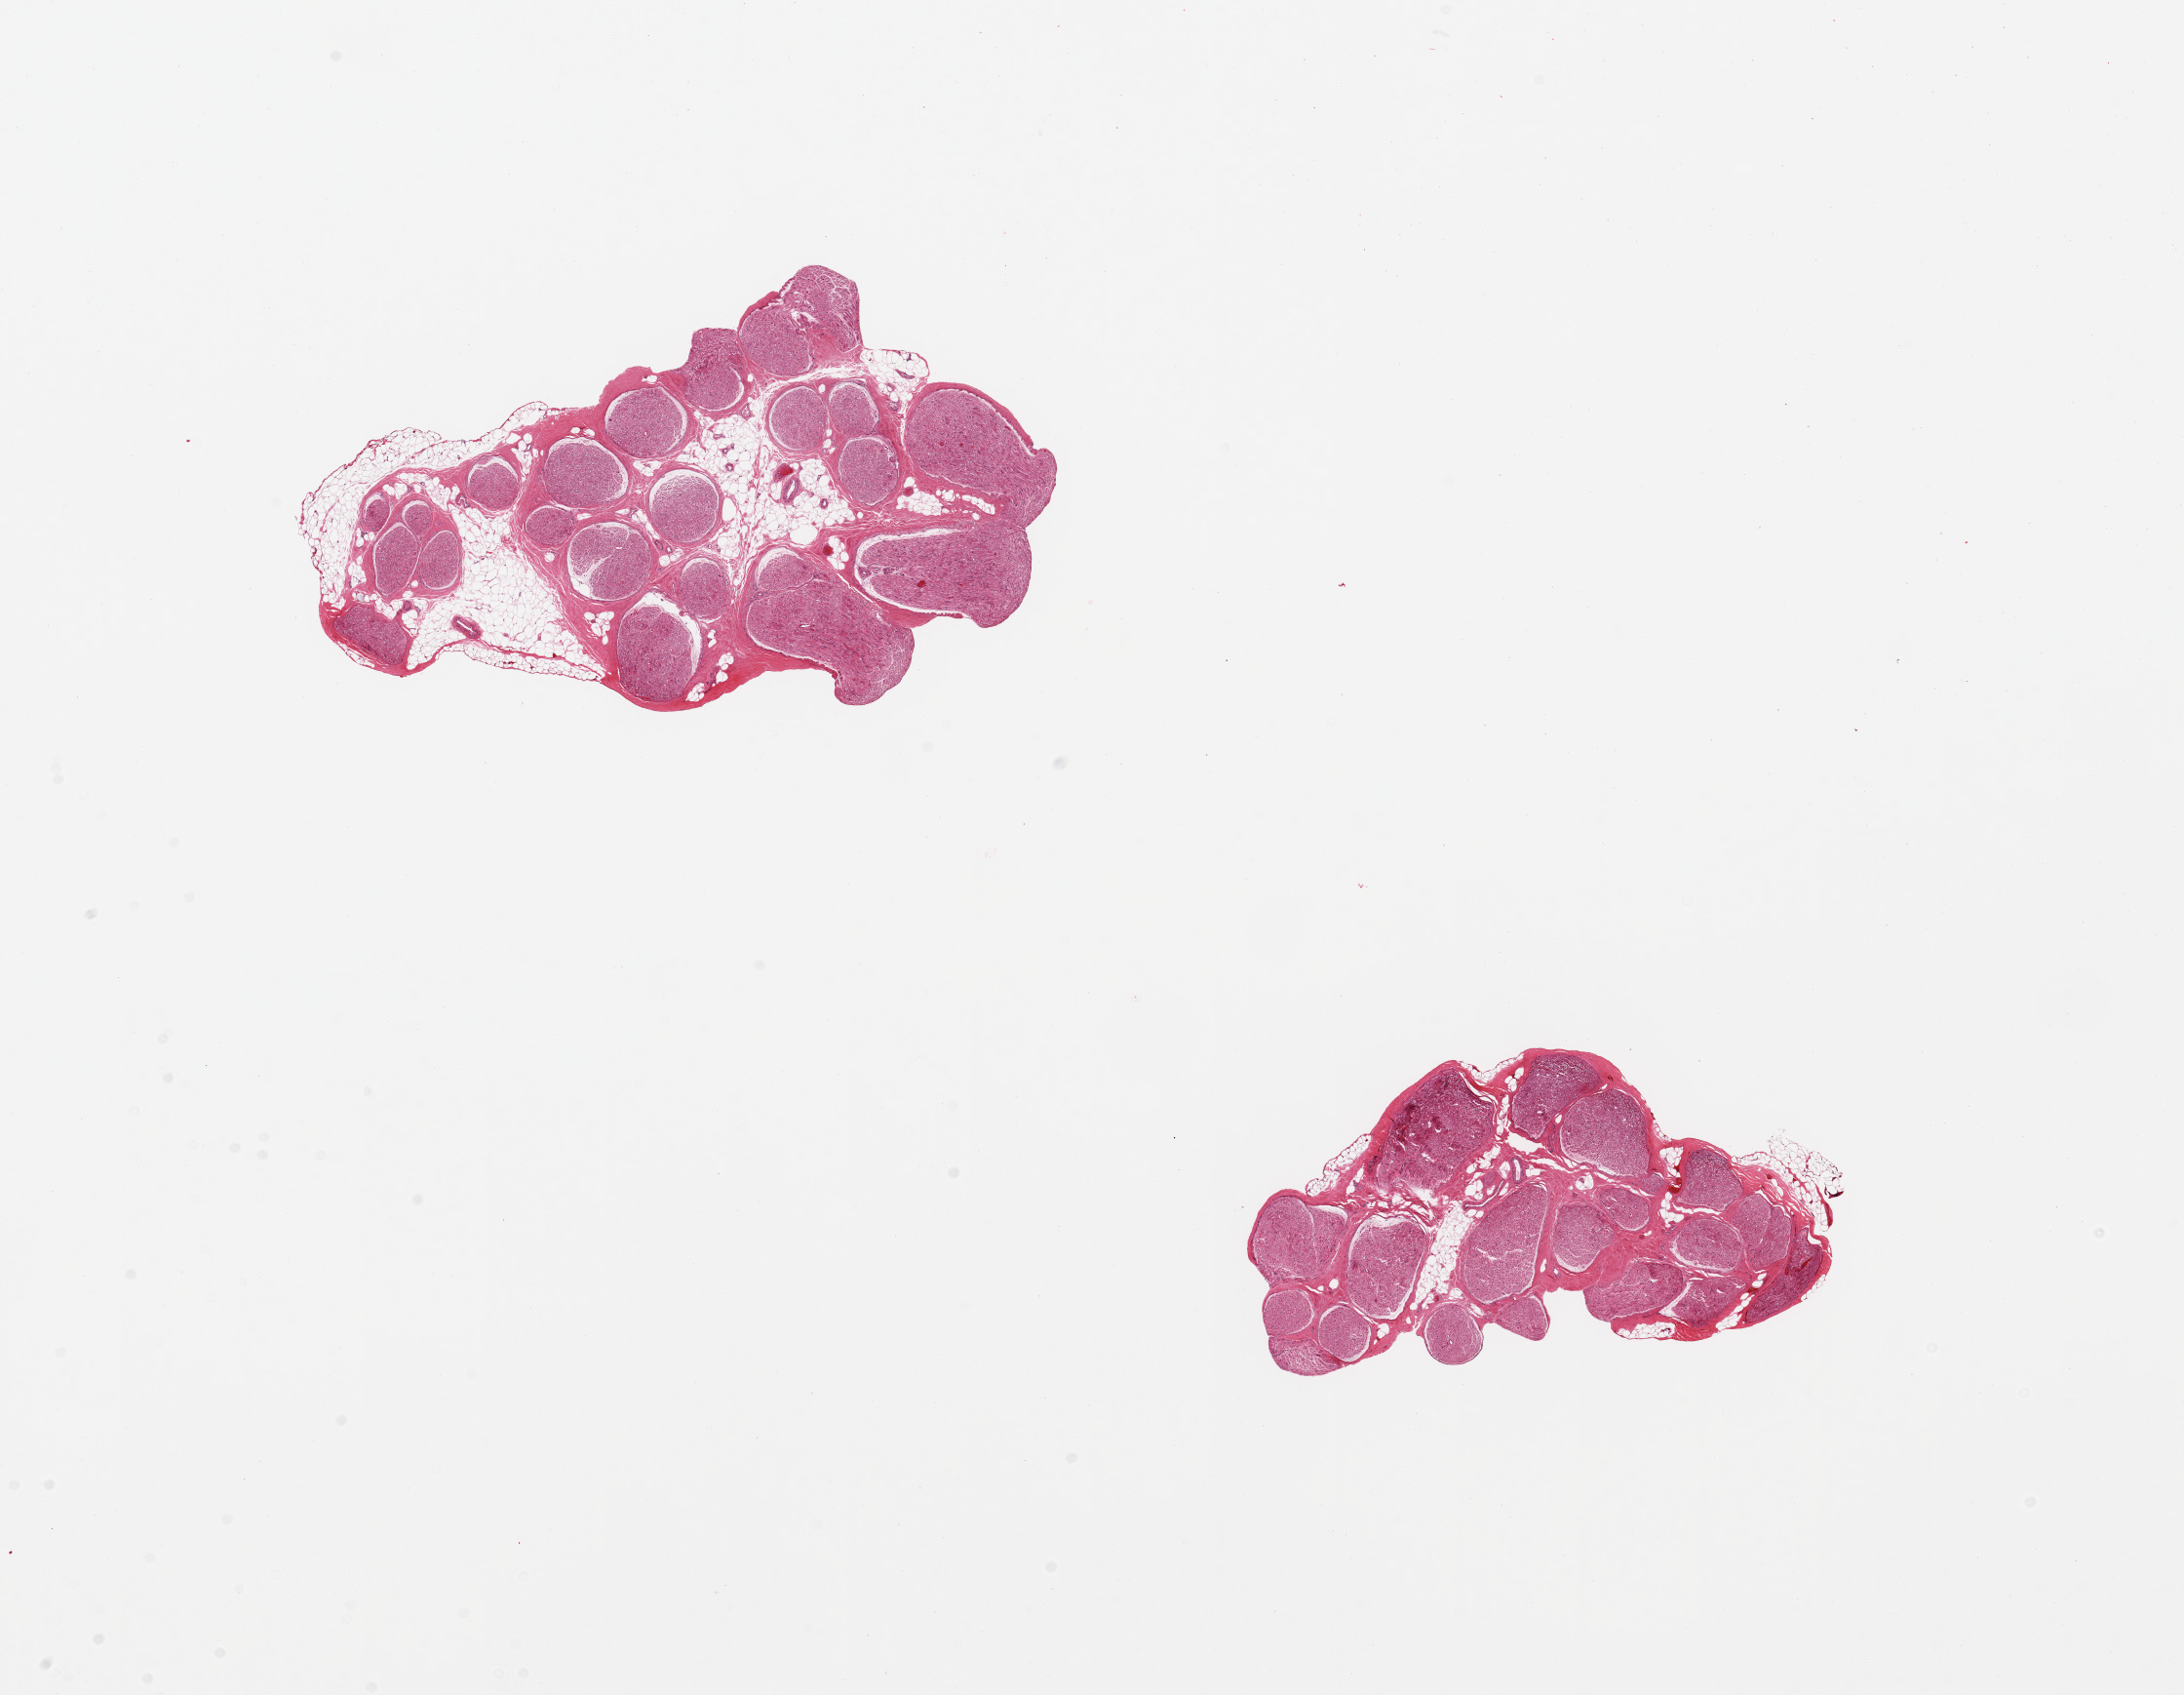
Digitized H&E-stained section, low-resolution overview of the scanned area, about 17.7 x 13.7 mm (slide scanned at 20x). PAXgene-fixed, paraffin-embedded tissue. Sampled site (target tissue): tibial nerve. Tissue donor sample. Male donor.
Reviewer comment on this tissue sample: 2 pieces; 20% & 10% internal fat.